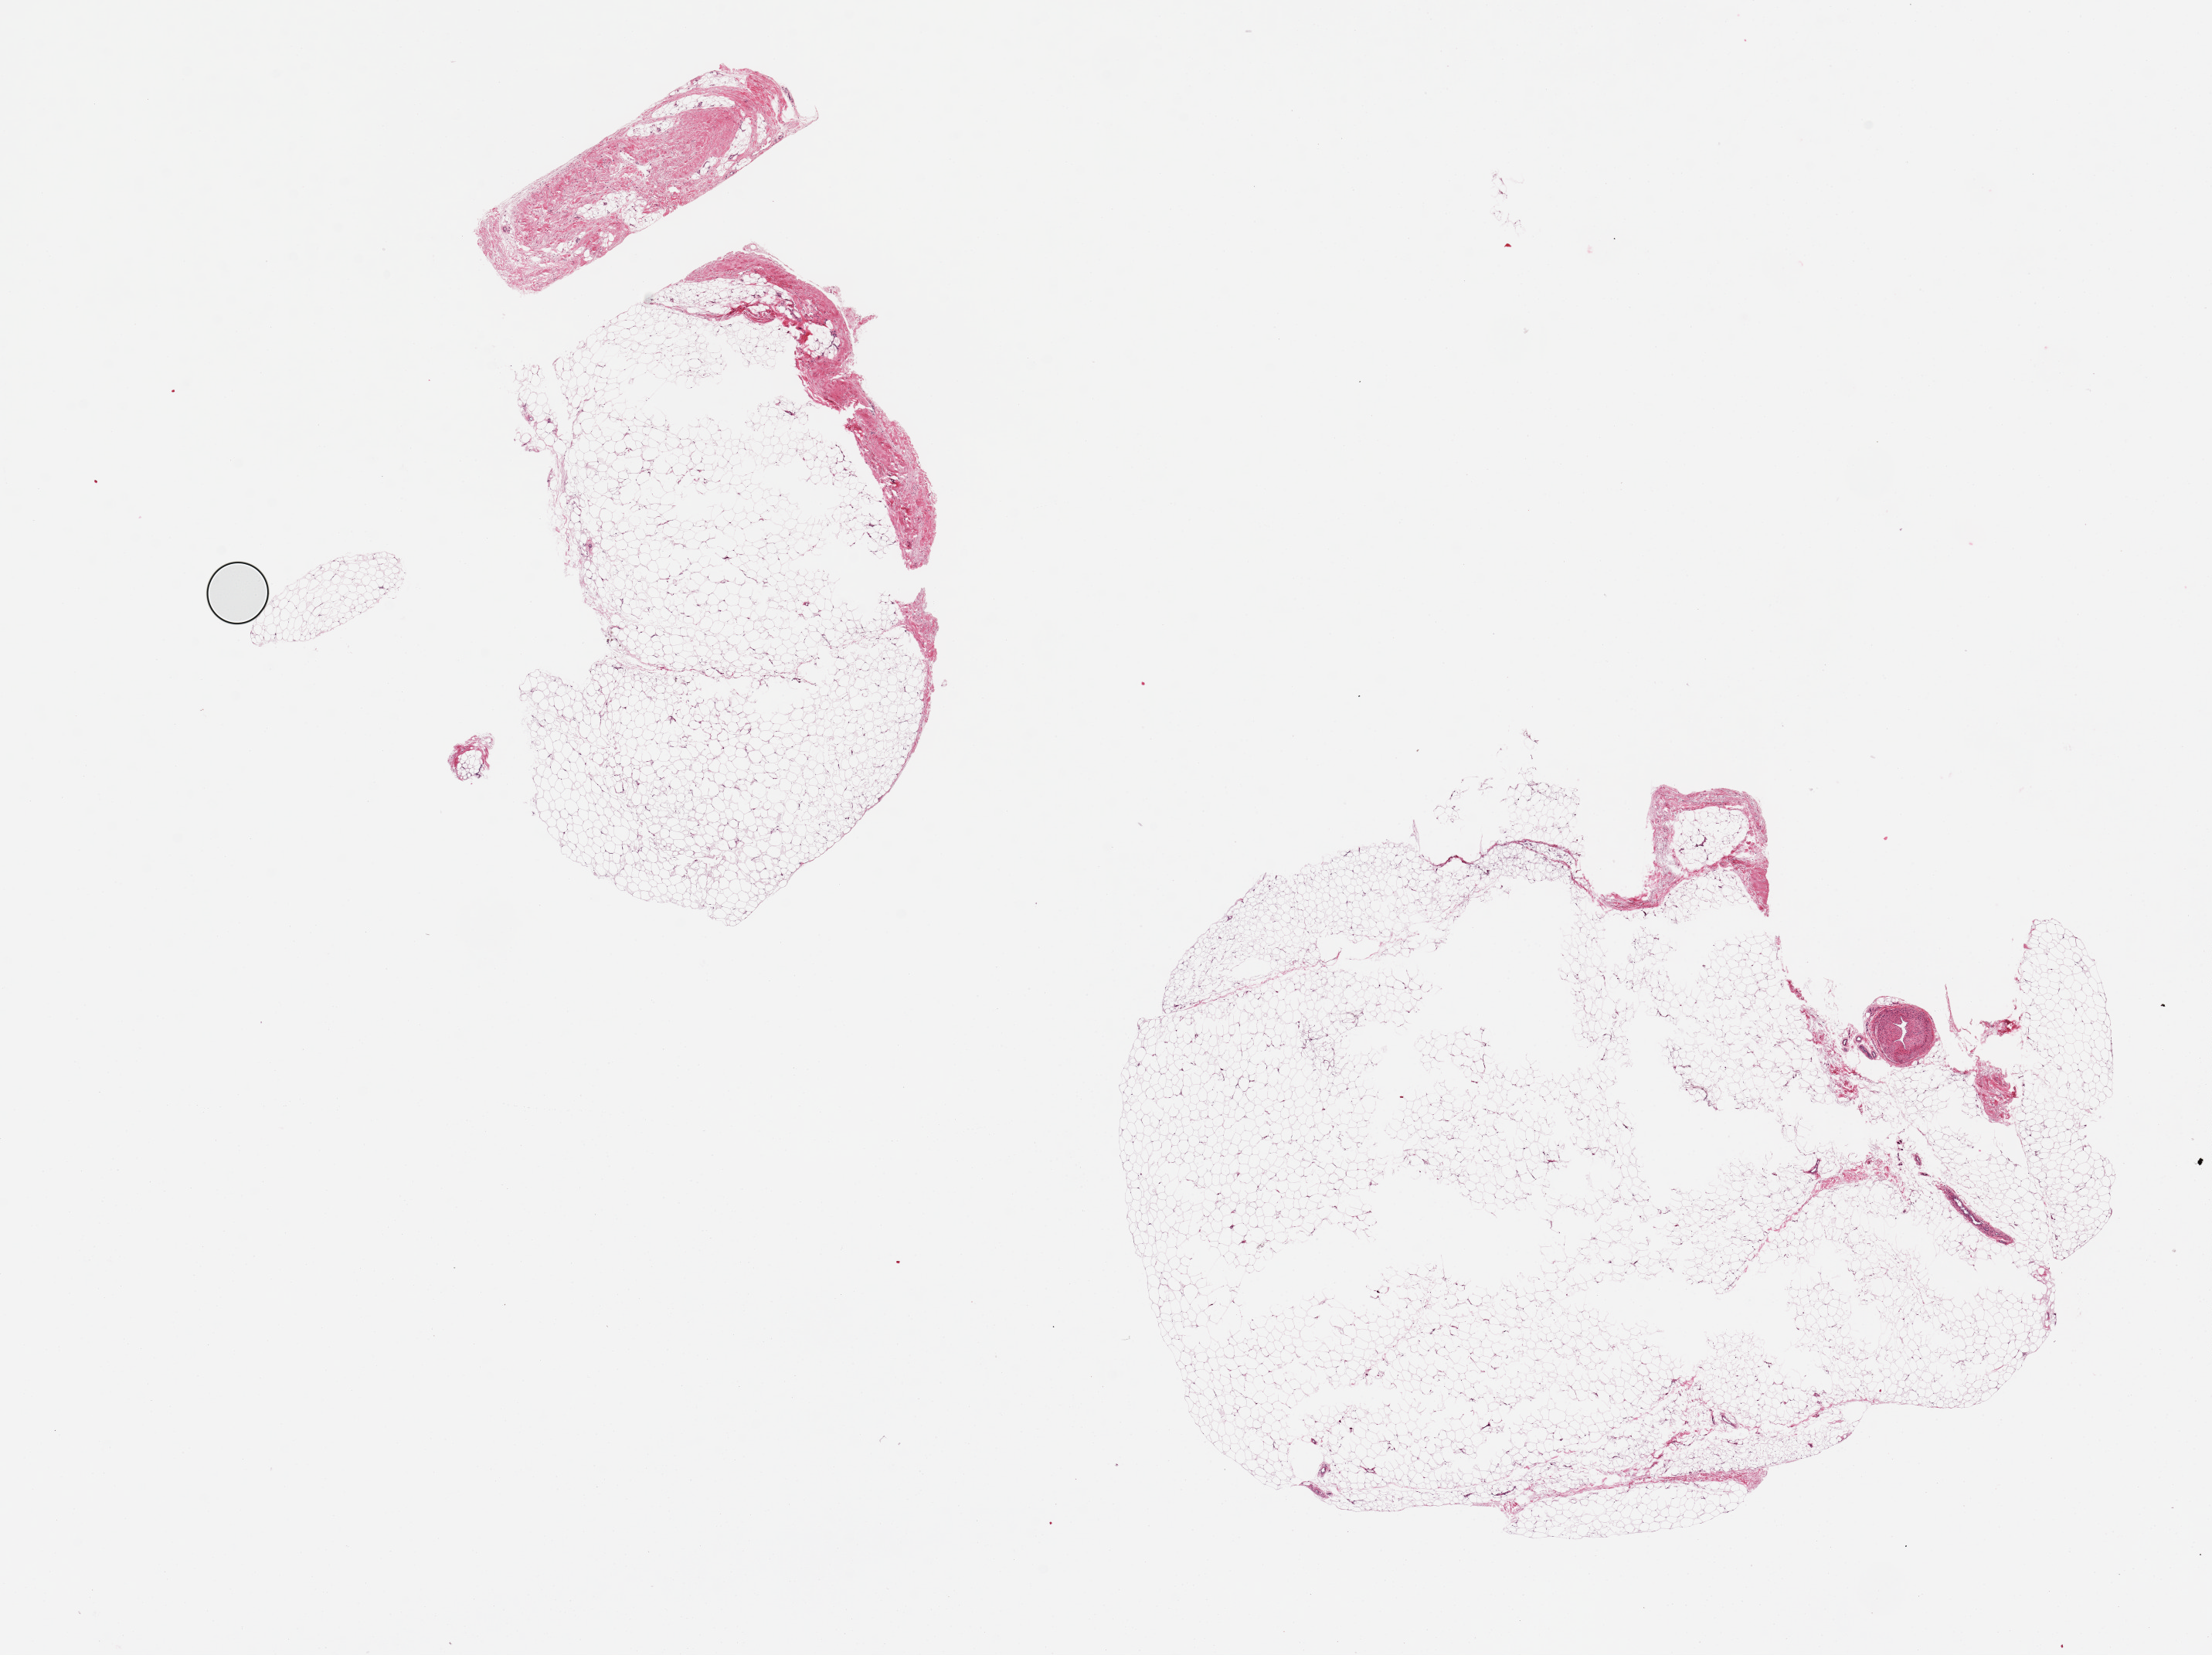
Whole-slide image, hematoxylin and eosin (H&E) stain, brightfield — shown as a low-resolution overview of the whole scanned area (about 22.6 x 16.9 mm, acquisition: 20x scan). PAXgene-fixed, paraffin-embedded tissue. Sampled site (target tissue): adipose tissue. Tissue donor sample. Donor: male.
Review note (as recorded): 2 pieces, one piece with central defect (poor fixation) and attached vessel, second piece is 10-20% fibroconnective tissue.